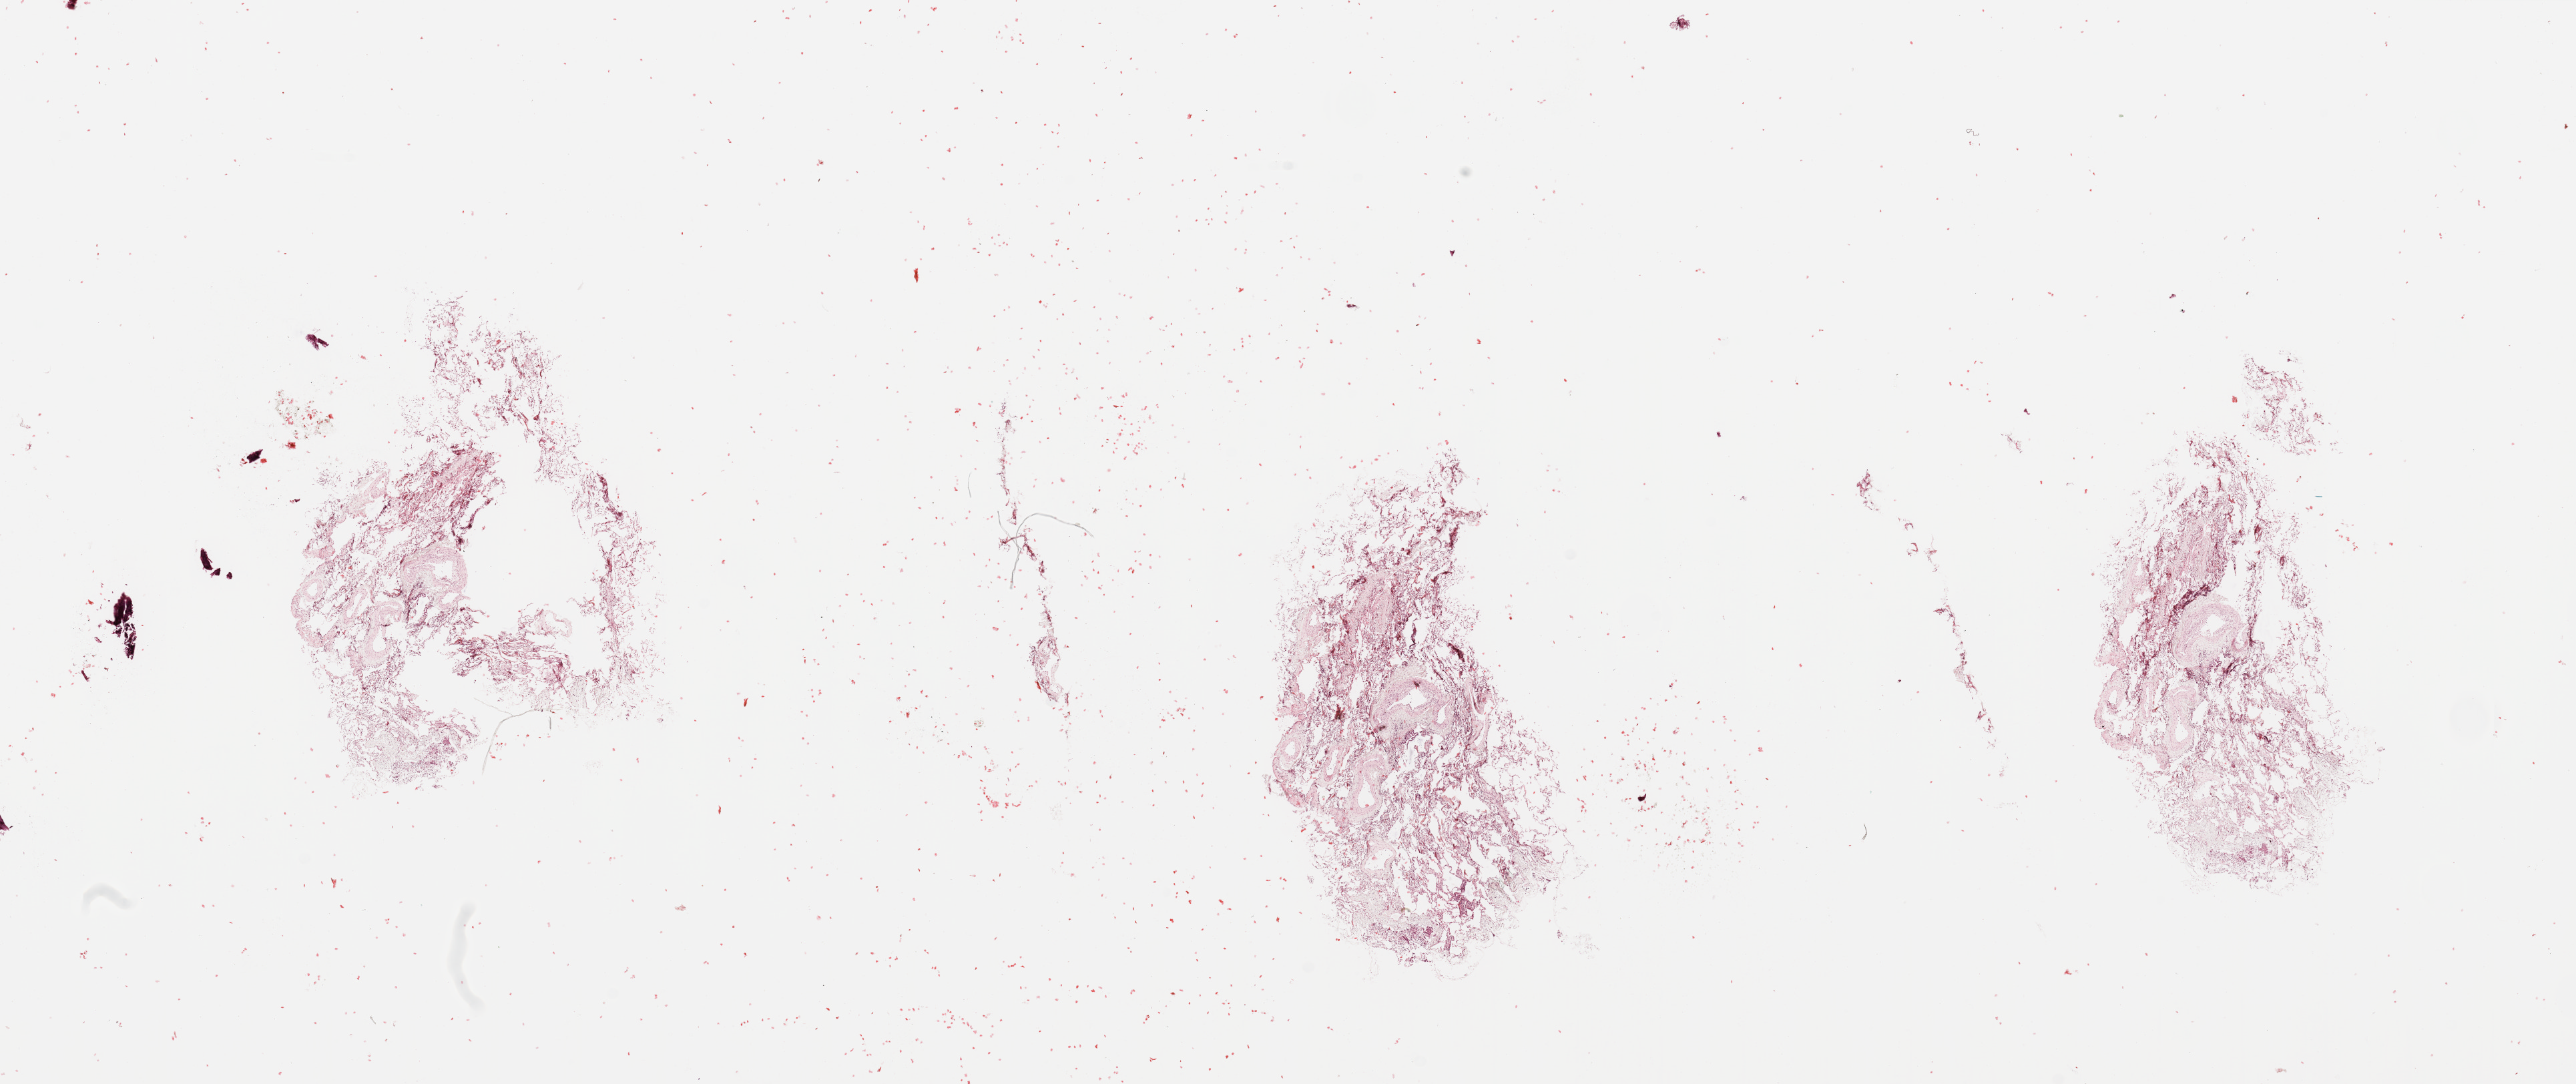
Digitized Hematoxylin and eosin (H&E) stained tissue section (whole slide), shown as a low-resolution overview of the whole scanned area (about 30.5 x 12.8 mm); normal (non-tumour) tissue sample, lung. 67-year-old male patient.
This section: normal (non-tumour) tissue from the same patient. Patient diagnosis: Squamous cell carcinoma, NOS.